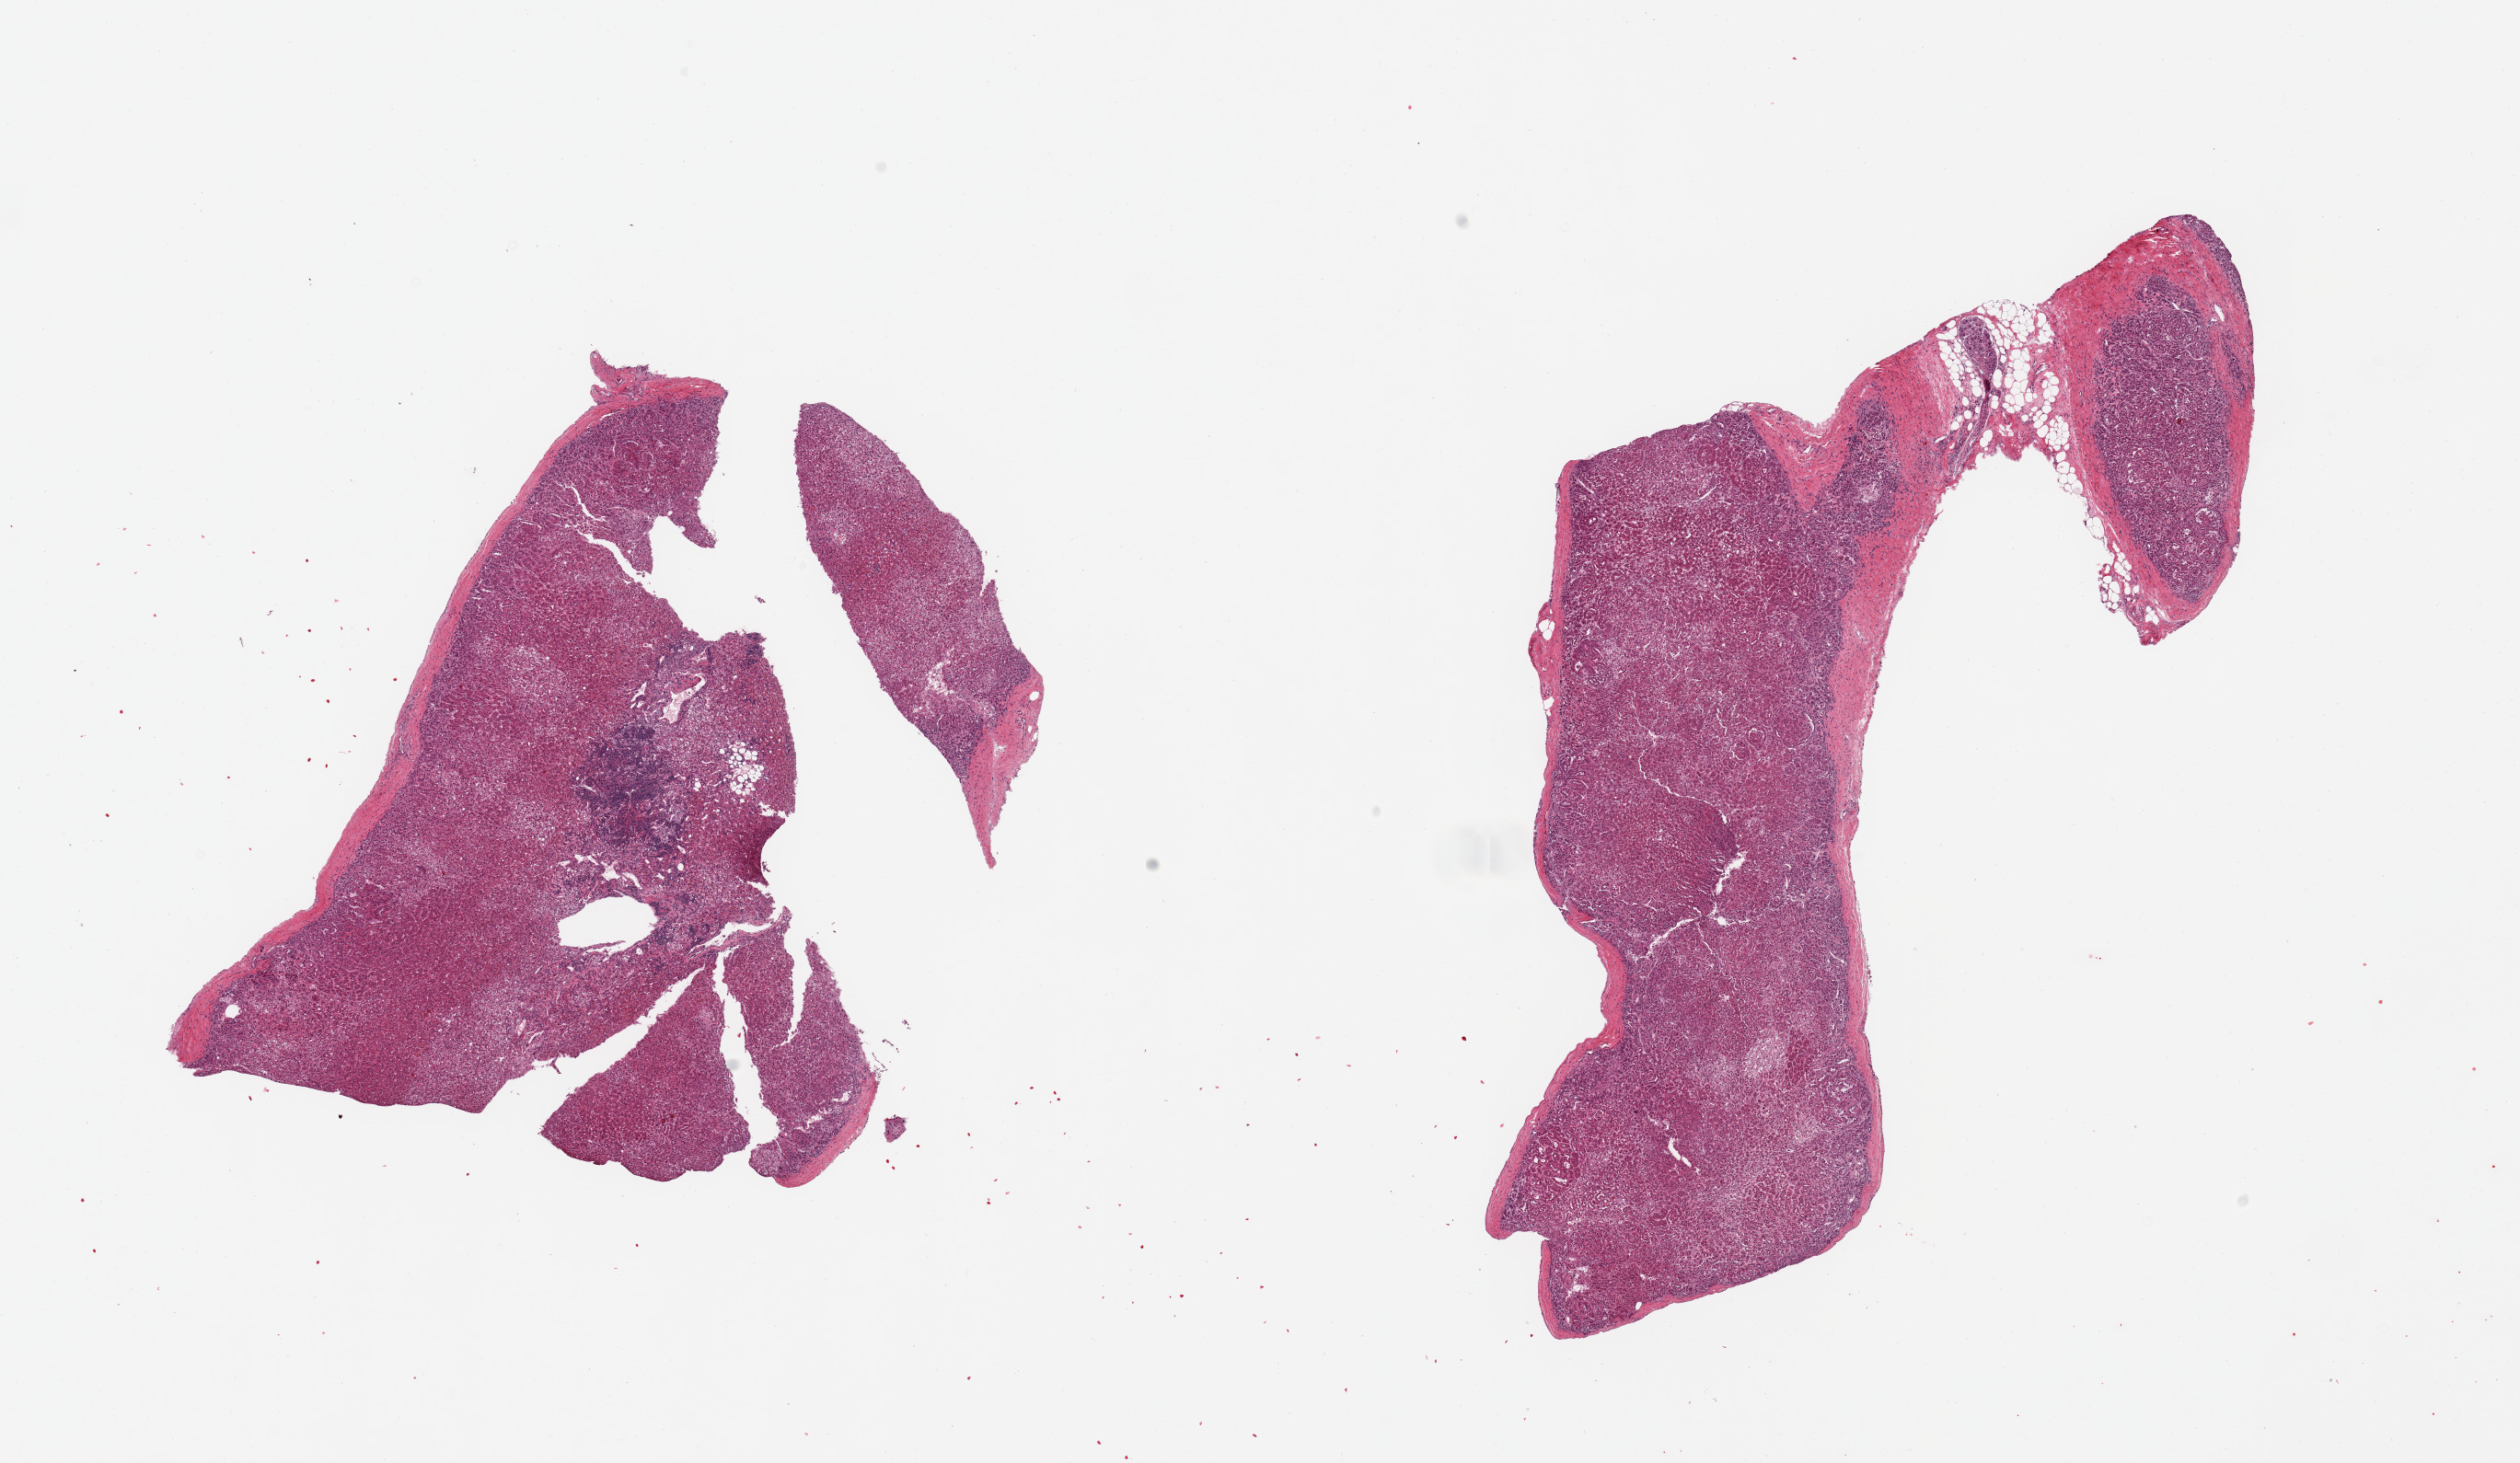
Hematoxylin and eosin (H&E) whole-slide image — a low-resolution overview of the entire scanned area, about 21.7 x 12.6 mm (acquisition: 20x scan). PAXgene-fixed paraffin-embedded (PFPE) section. Section of adrenal gland (target tissue). Donor tissue sample. Donor: male.
Pathologist's review note for this sample: 2 pieces, cortex, ~1mm focus of well-preserved medulla.